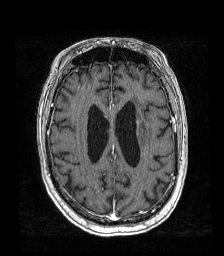
Brain MRI from a brain-tumour surgery series, one axial slice. Slice 61 of 192 in the series (ordered by position). T1-weighted post-contrast. 1 mm slice thickness. 224 × 256 image matrix, field of view 219 × 250 mm. From the clinical record (not read from this slice): histopathology: Metastatic carcinoma from lung primary; tumour location: Left Frontal Caudate.
Outlined on this slice (manually delineated by an expert):
- tumour: bounding box (x1, y1, x2, y2) in pixels: (136, 120, 141, 133)